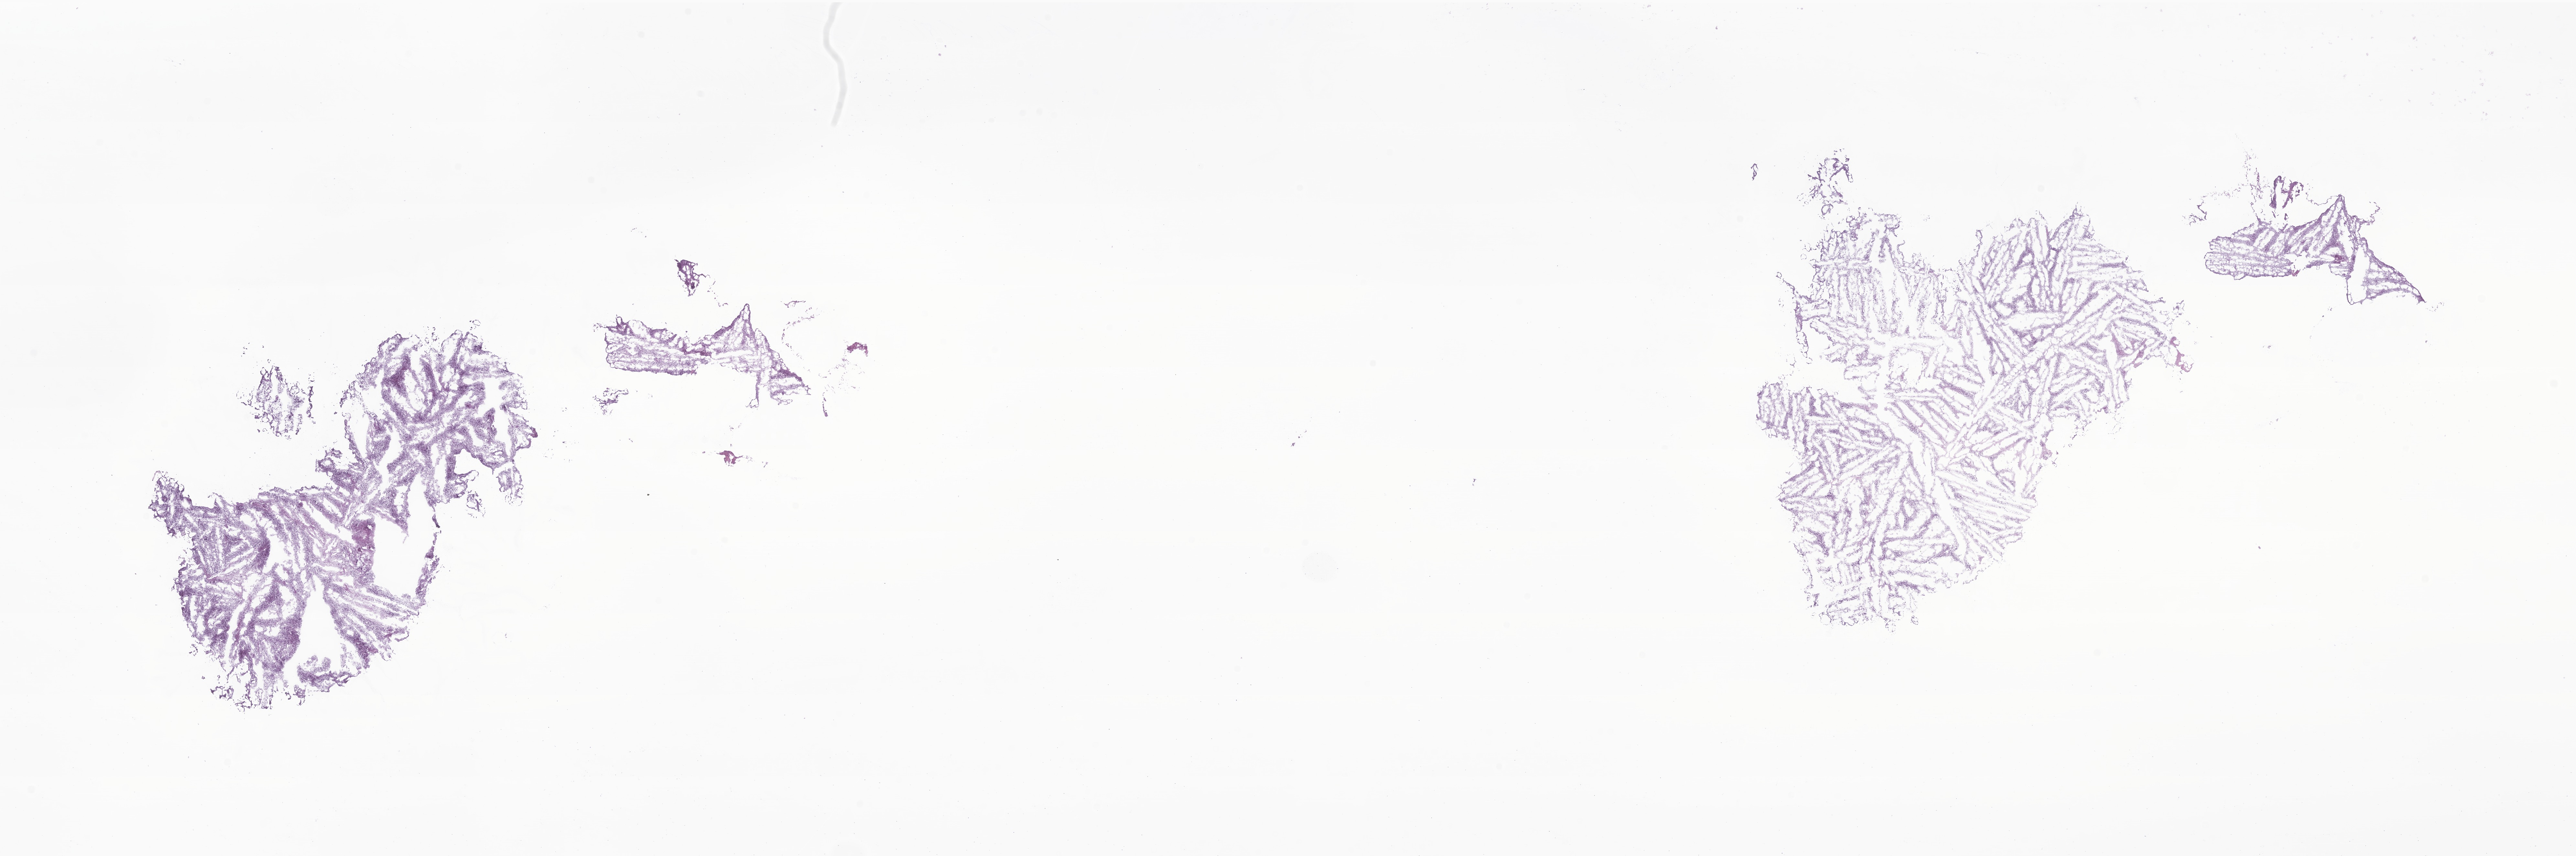
Whole-slide image, hematoxylin and eosin (H&E) stain of tumor tissue from the spinal cord — low-resolution overview of the scanned area, about 33.6 x 11.2 mm; frozen section. Male patient, age 86 months.
- diagnosis (ICD-O-3 morphology term): Neoplasm, uncertain whether benign or malignant